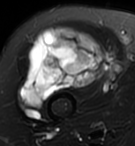
MRI of an extremity soft-tissue mass, one axial slice. Slice 68 of 95 in the series (ordered by position). T2-weighted fat-saturated. MR volume resampled by the dataset authors to the PET/CT grid (not the native acquisition matrix). 3.27 mm slice thickness. 135 × 146 image matrix, field of view 132 × 143 mm. Female patient. From the clinical record (not read from this slice): histological type: pleiomorphic undifferentiated sarcoma; grade: high; site of the primary tumour: right quadricep.
Annotated regions visible in this slice (expert contour drawn on MRI and transferred to this co-registered scan by the dataset authors):
- gross tumour volume including surrounding oedema: bounding box (x1, y1, x2, y2) in pixels: (21, 25, 104, 108)
- gross tumour volume (mass): (21, 25, 104, 108)